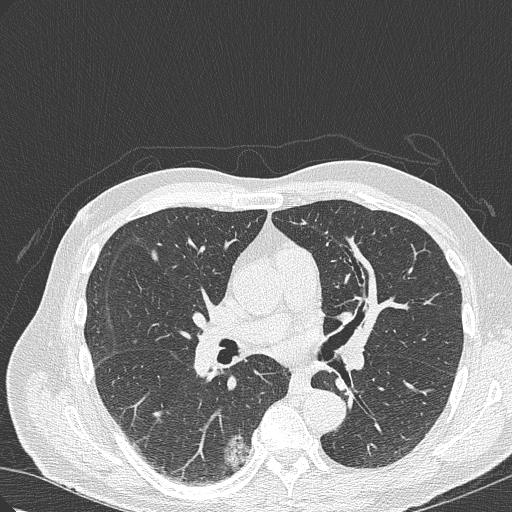
Axial slice from a low-dose chest CT screening exam. Baseline screening round. Lung window (W 1500 / L -600 HU). Lung (sharp) reconstruction kernel (B50f). Slice 143 of 322 in the series. 512 × 512 image matrix. Male, age 70 years at enrolment. Current smoker at enrolment.
• Expert-annotated lung lesion, box from (x=198, y=419) to (x=261, y=478) px.
• The screening reader recorded 4 non-calcified nodules or masses ≥4 mm on this exam (right lower lobe, right lower lobe, right upper lobe, right lower lobe); which of them this box marks is not recorded.
• Official screen result: positive, change unspecified: nodule(s) >= 4 mm or enlarging nodule(s), mass(es), or other non-specific abnormalities suspicious for lung cancer.
• Lung cancer was diagnosed 978 days after this screen: bronchiolo-alveolar adenocarcinoma, NOS, right lower lobe, poorly differentiated (G3), stage IB (AJCC 6th edition), 30 mm at pathology.